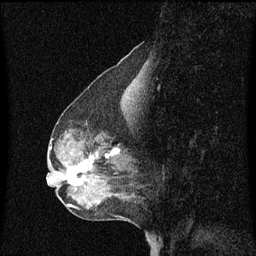
Breast MRI (dynamic contrast-enhanced), one sagittal slice. Slice 25 of 60 in the series (ordered by position). Dynamic contrast-enhanced series, image 2 of 3 at this slice position (ordered by acquisition). 1.5 T. TE 4.2 ms, TR 8.4 ms. 2 mm slice thickness. 256 × 256 image matrix, field of view 200 × 200 mm. Female patient, age 50 years. Case-level facts recorded for this patient, not image findings: setting: breast cancer imaged before/during neoadjuvant chemotherapy; receptor status: HR-positive, HER2-negative.
Outlined on this slice (semi-automatically segmented with operator editing):
- analysis volume of interest (the breast-tissue region the enhancement analysis was run in; not a lesion): bounding box (x1, y1, x2, y2) in pixels: (61, 144, 129, 189)
- tumour enhancement mask (voxels above the 70 % enhancement threshold inside the analysis volume of interest): (68, 150, 120, 185)